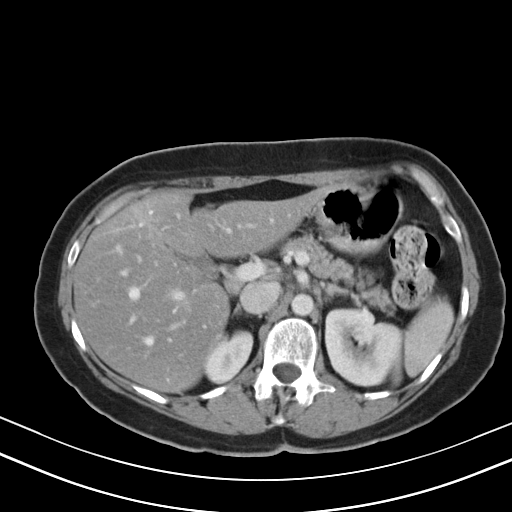
Contrast-enhanced abdominal CT, one axial slice. Position 28 of 47 along the scan axis. Reconstruction kernel B40s. 130 kVp. Intravenous contrast given. Soft-tissue window (W 400 / L 40 HU). 5 mm slice thickness. 512 × 512 image matrix, field of view 350 × 350 mm. Female patient. Case-level facts recorded for this patient, not image findings: diagnosis: colorectal cancer liver metastases, imaged before liver resection; multiple liver metastases: no; largest metastasis: 3.5 cm; disease in both lobes: no.
Annotated regions visible in this slice (outlined manually by an expert reader):
- hepatic veins: box from (x=123, y=211) to (x=229, y=344) px
- liver: (x=75, y=194)–(x=315, y=392)
- planned liver remnant (the part of the liver to remain after resection): (x=75, y=194)–(x=314, y=392)
- portal vein (with intrahepatic branches): (x=128, y=288)–(x=191, y=328)